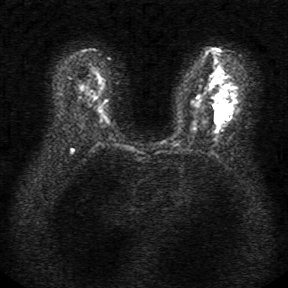
Breast MRI, one axial slice; slice 21 of 34 in the series (ordered by position); diffusion-weighted series; image 2 of 4 stored at this slice position (different b-values; order by instance number); 1.5 T; 5 mm slice thickness; 288 × 288 image matrix, field of view 340 × 340 mm. Female patient.
Annotated regions visible in this slice (expert manual segmentation):
- tumour on diffusion-weighted imaging: bounding box <214,110,228,122> (left, top, right, bottom; pixels)